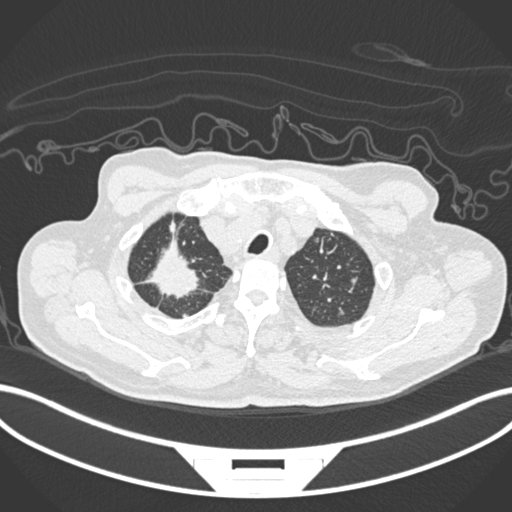
Chest CT, one axial slice; position 190 of 207 along the scan axis; reconstruction kernel B30f; lung window (W 1500 / L -600 HU); 512 × 512 image matrix. Male patient, age 69 years. Case-level facts recorded for this patient, not image findings: clinical TNM (as recorded): T1c N1 M1.
Structures marked on this image (bounding box drawn by a radiologist):
- lung tumour (recorded histology: adenocarcinoma): bounding box <137,239,205,300> (left, top, right, bottom; pixels)